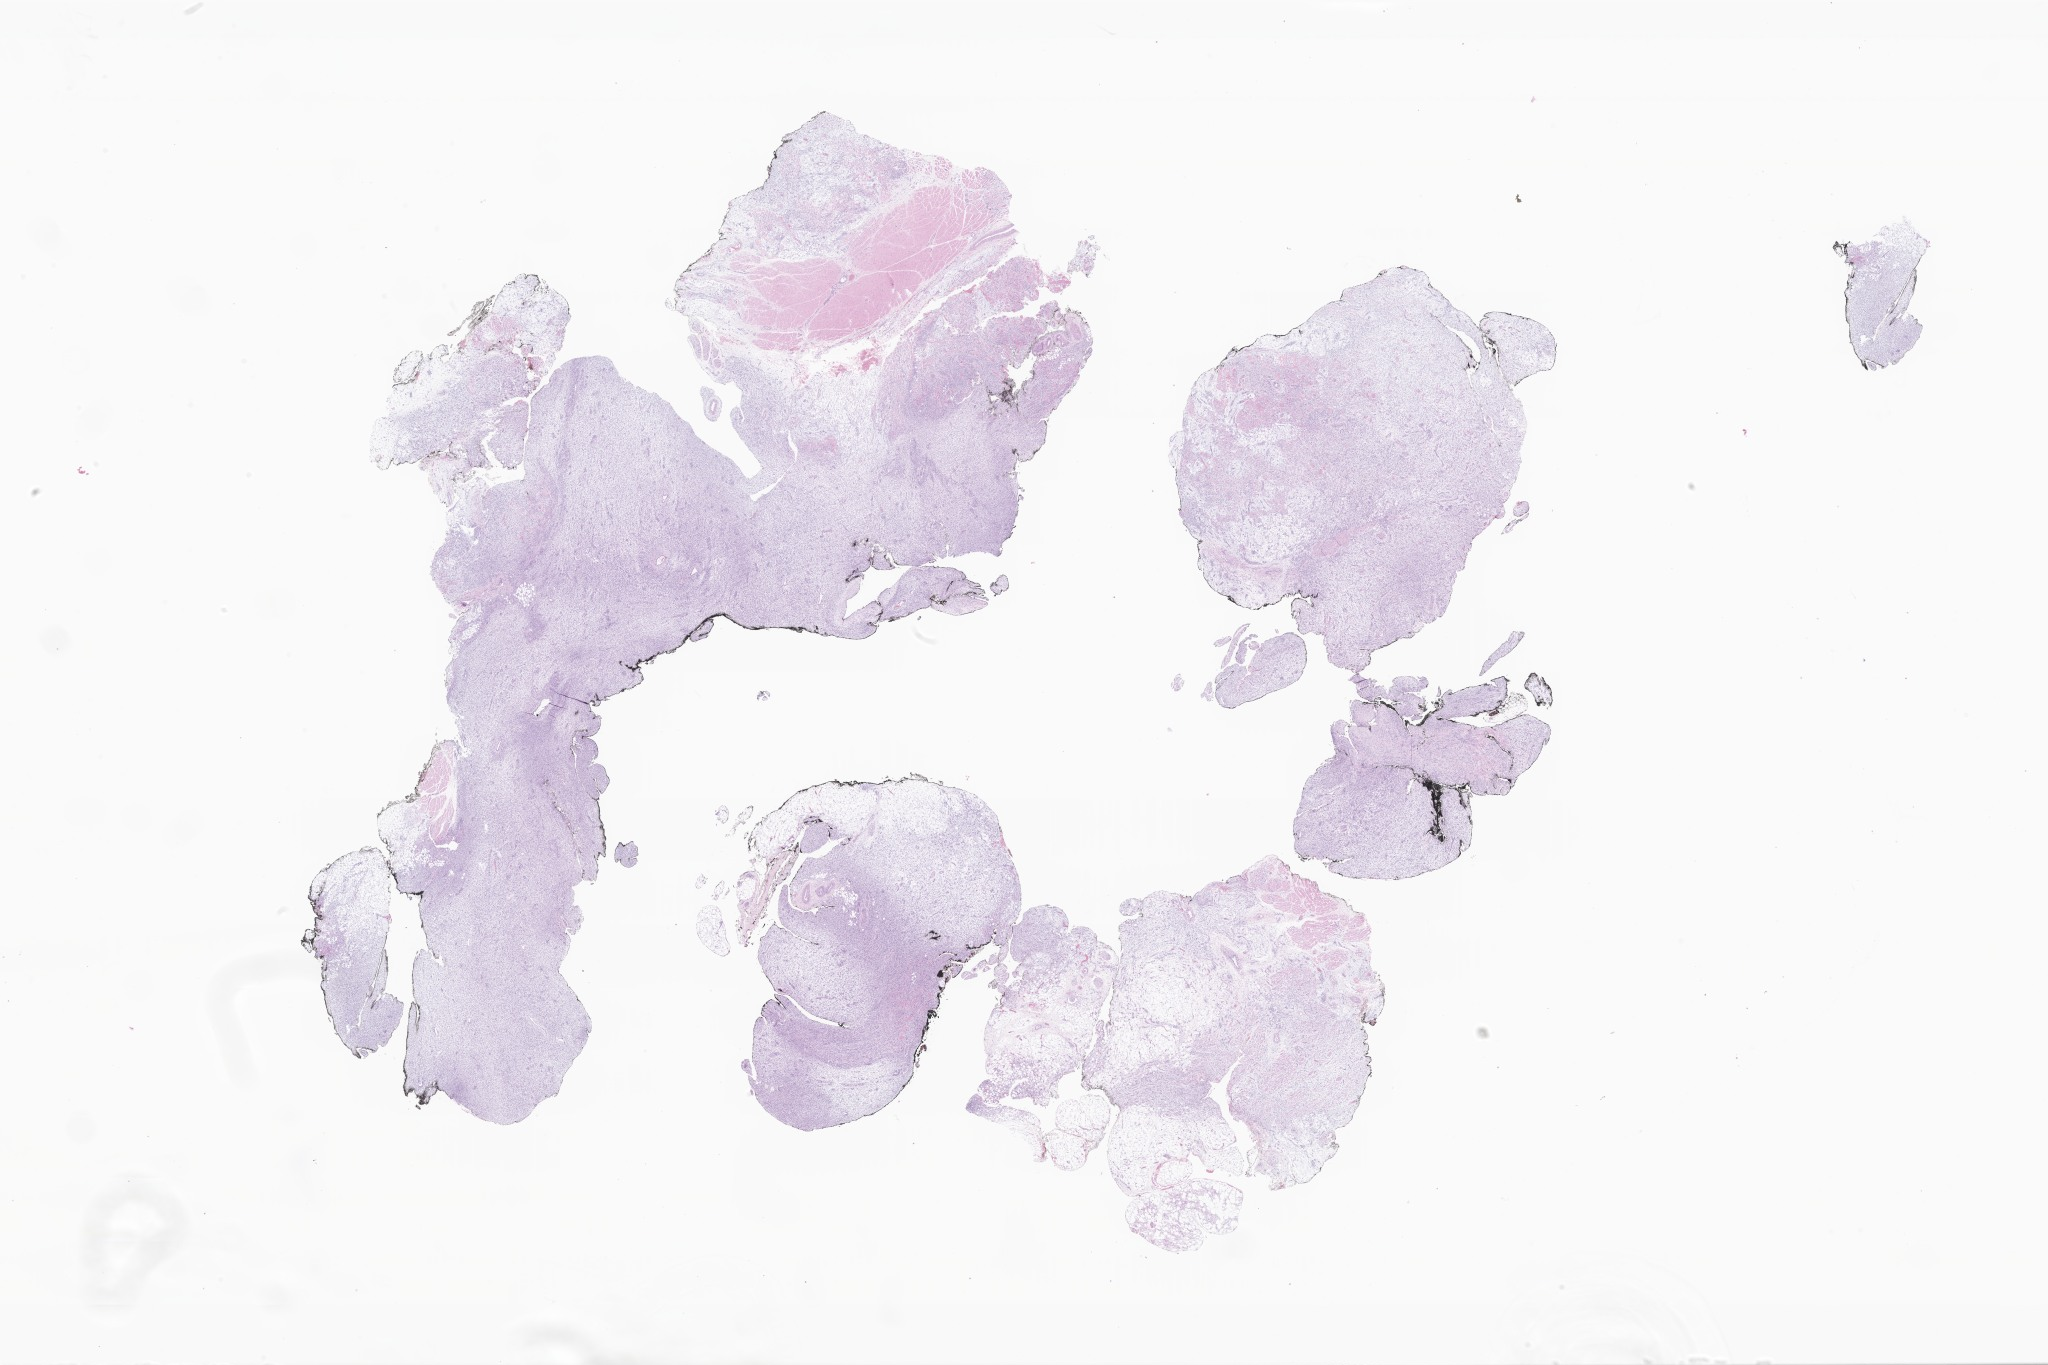
Digitized haematoxylin and eosin-stained section of tumor tissue from the soft tissue — shown as a low-resolution overview of the whole scanned area (about 34.5 x 23.0 mm). Formalin-fixed, paraffin-embedded (FFPE) tissue. Patient male; age 82 days.
Recorded diagnosis: Infantile fibrosarcoma.